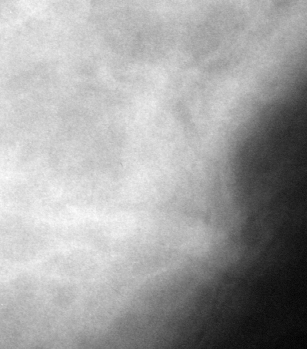
Region of interest cut from a scanned film mammogram (one marked finding); left breast; MLO view.
Finding: mass, shape round, margins obscured; BI-RADS assessment category 4; subtlety rating 2 on a 1 (subtle) to 5 (obvious) scale; pathology (as recorded): benign.